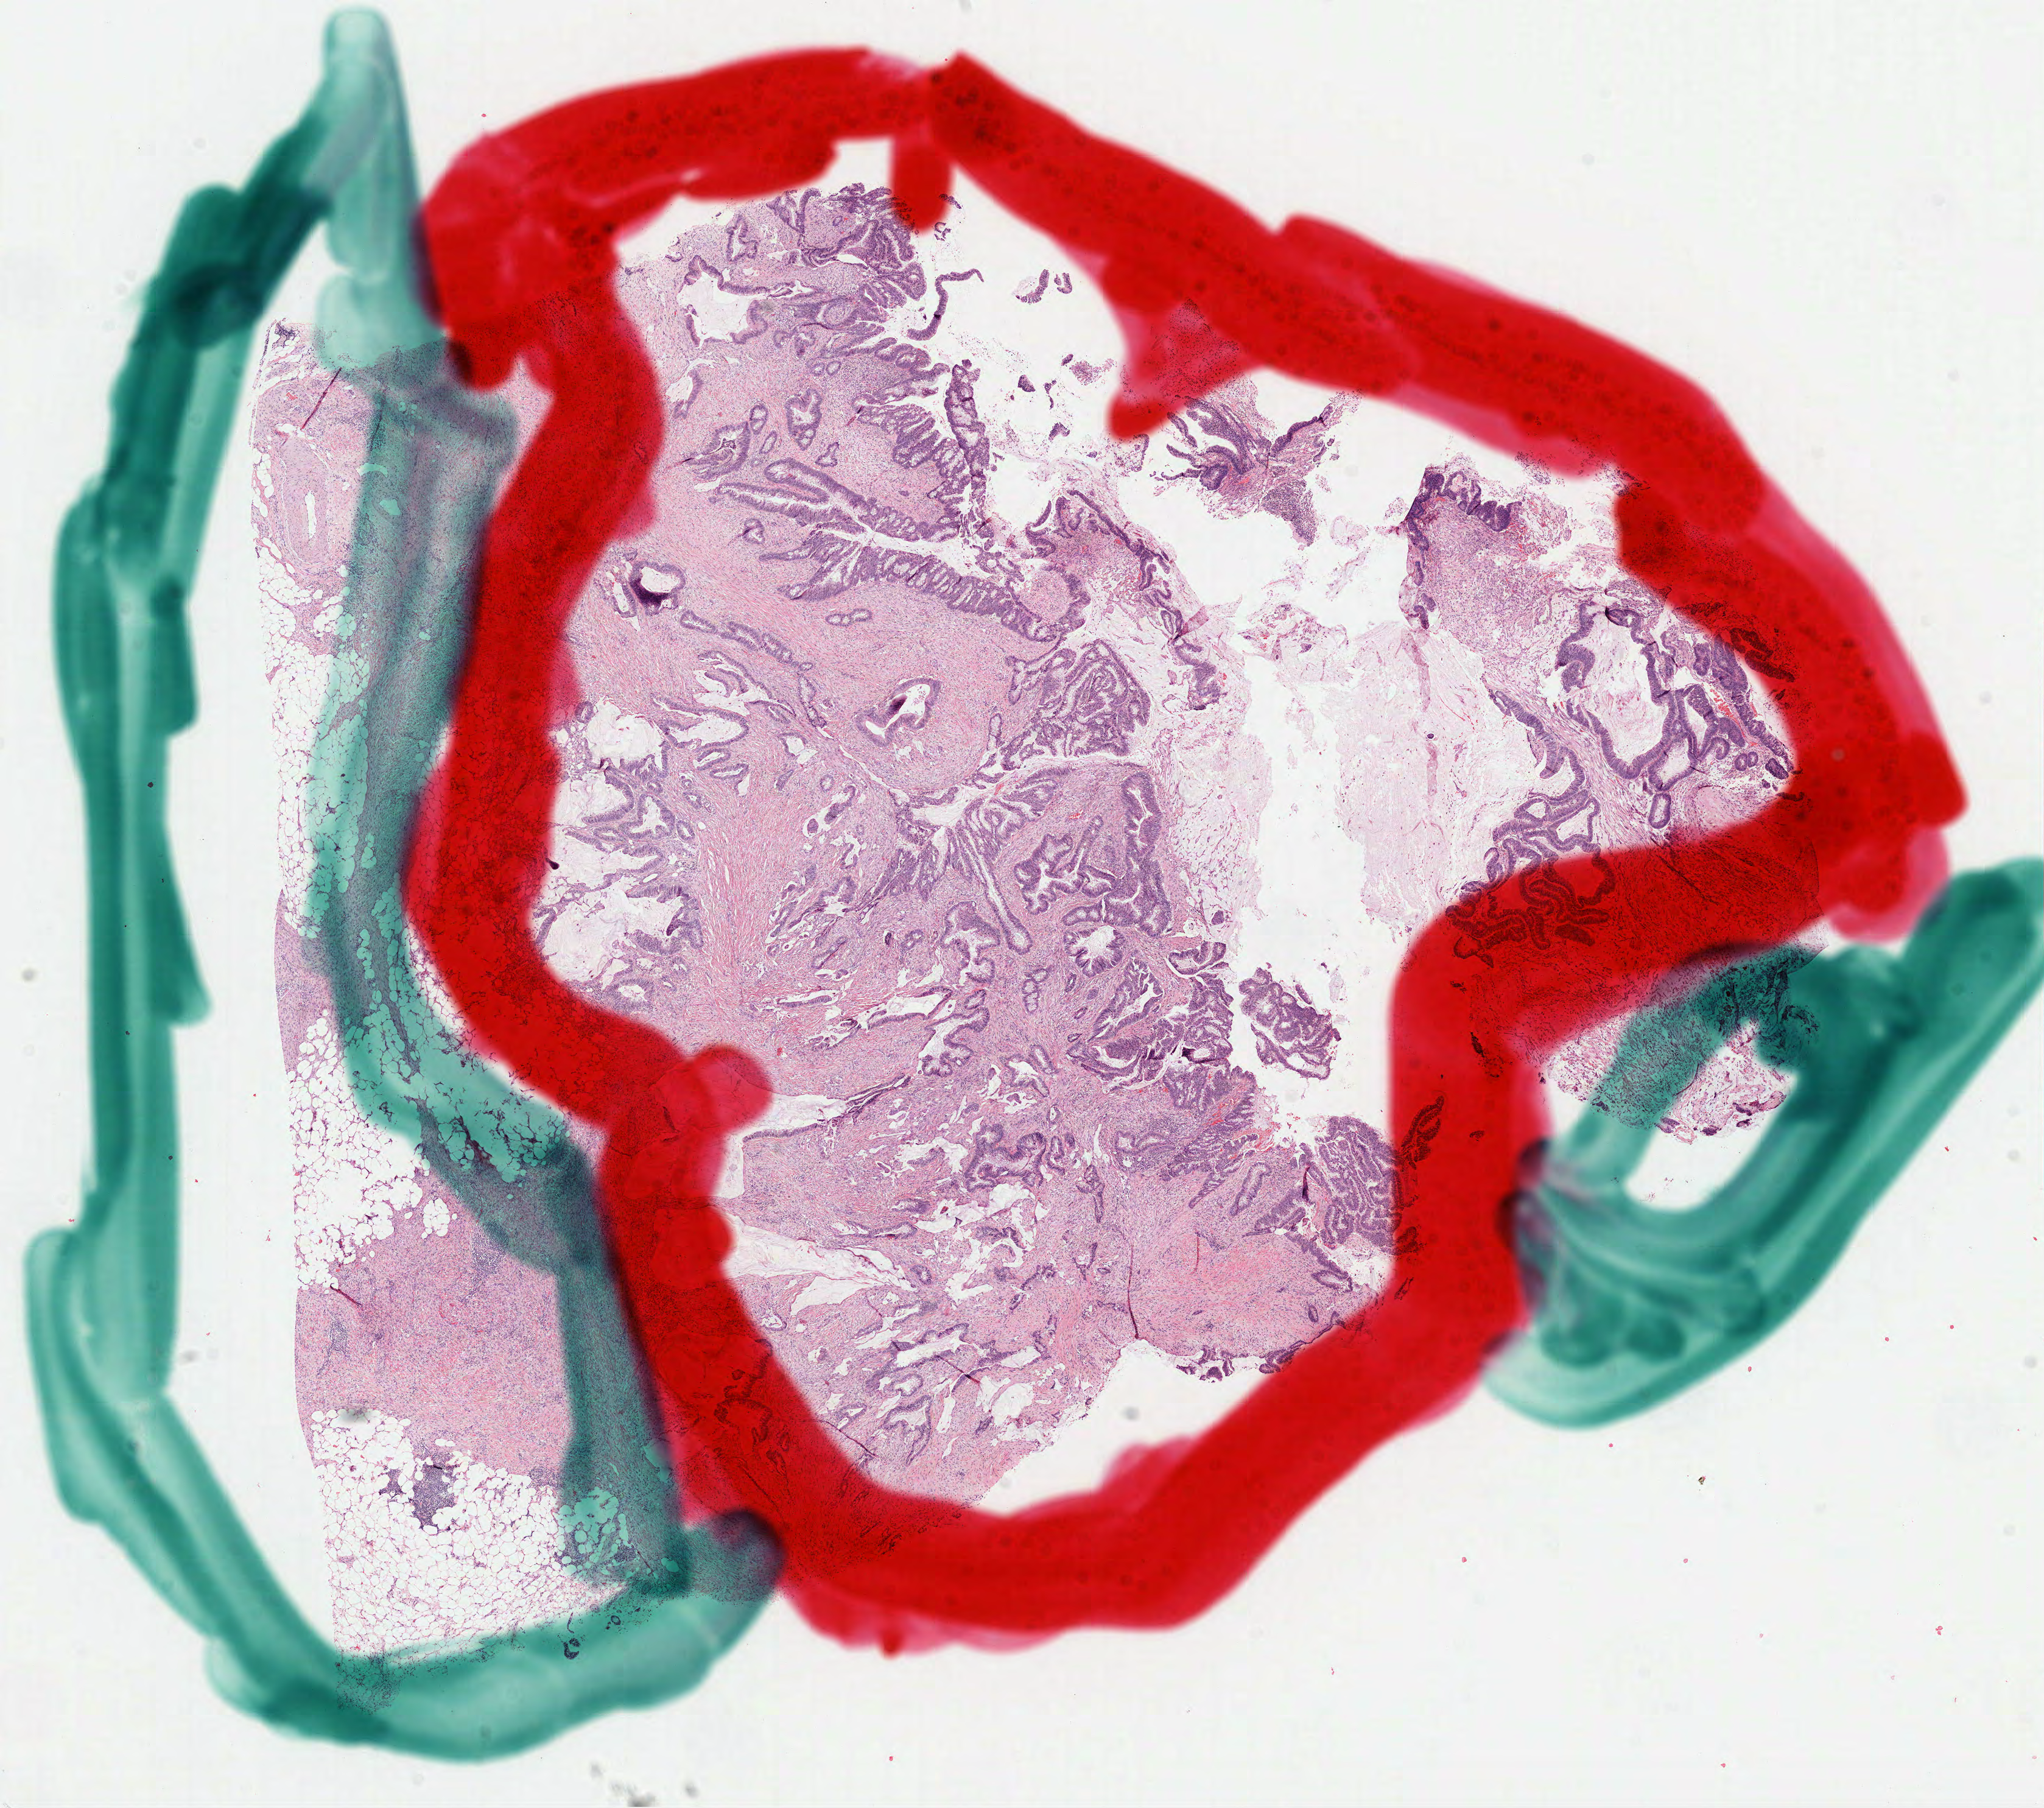
H&E whole-slide image — shown as a low-resolution overview of the whole scanned area (about 13.5 x 12.0 mm, slide scanned at 40x); formalin-fixed paraffin-embedded (FFPE) diagnostic section; sample: primary tumour, colon. Female, age 70 years at initial diagnosis.
Lymph nodes positive (case pathology): 0 of 12 examined. AJCC pathologic stage: IIA (7th edition). Histologic diagnosis: Adenocarcinoma, NOS (sigmoid colon).